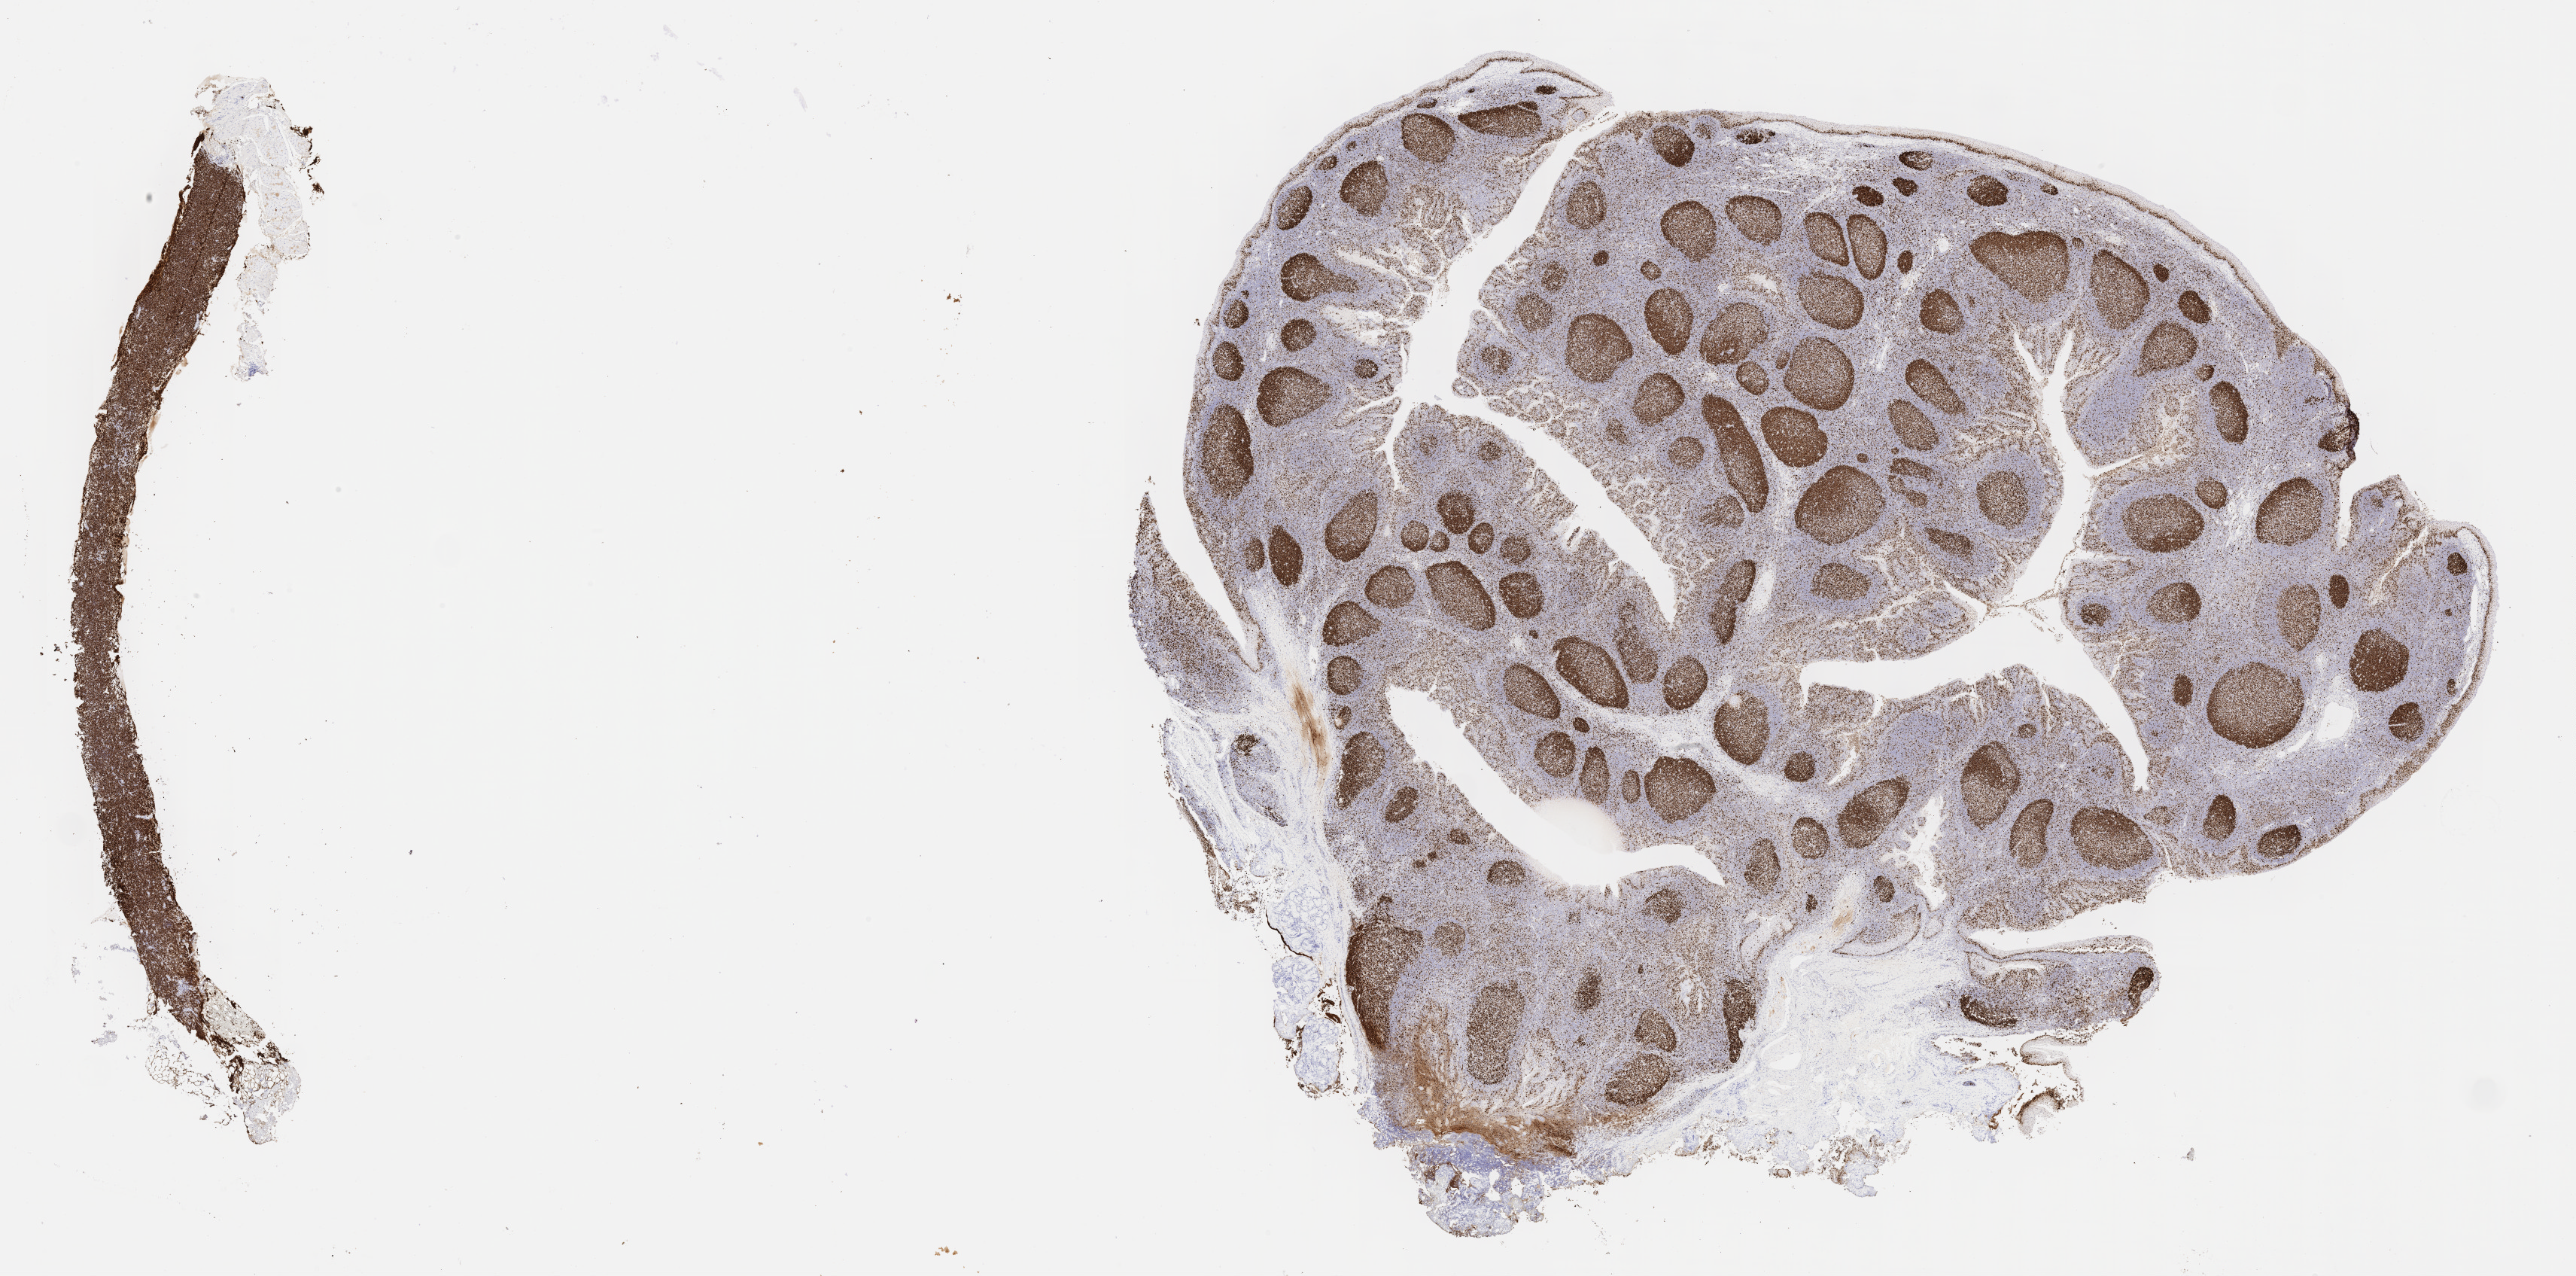
IHC for Ki-67, whole-slide image — low-resolution overview of the scanned area, about 27.7 x 13.7 mm. Tumor tissue. Site: cranium. Female patient; age at initial diagnosis 7 years.
- histologic diagnosis: Burkitt lymphoma, NOS